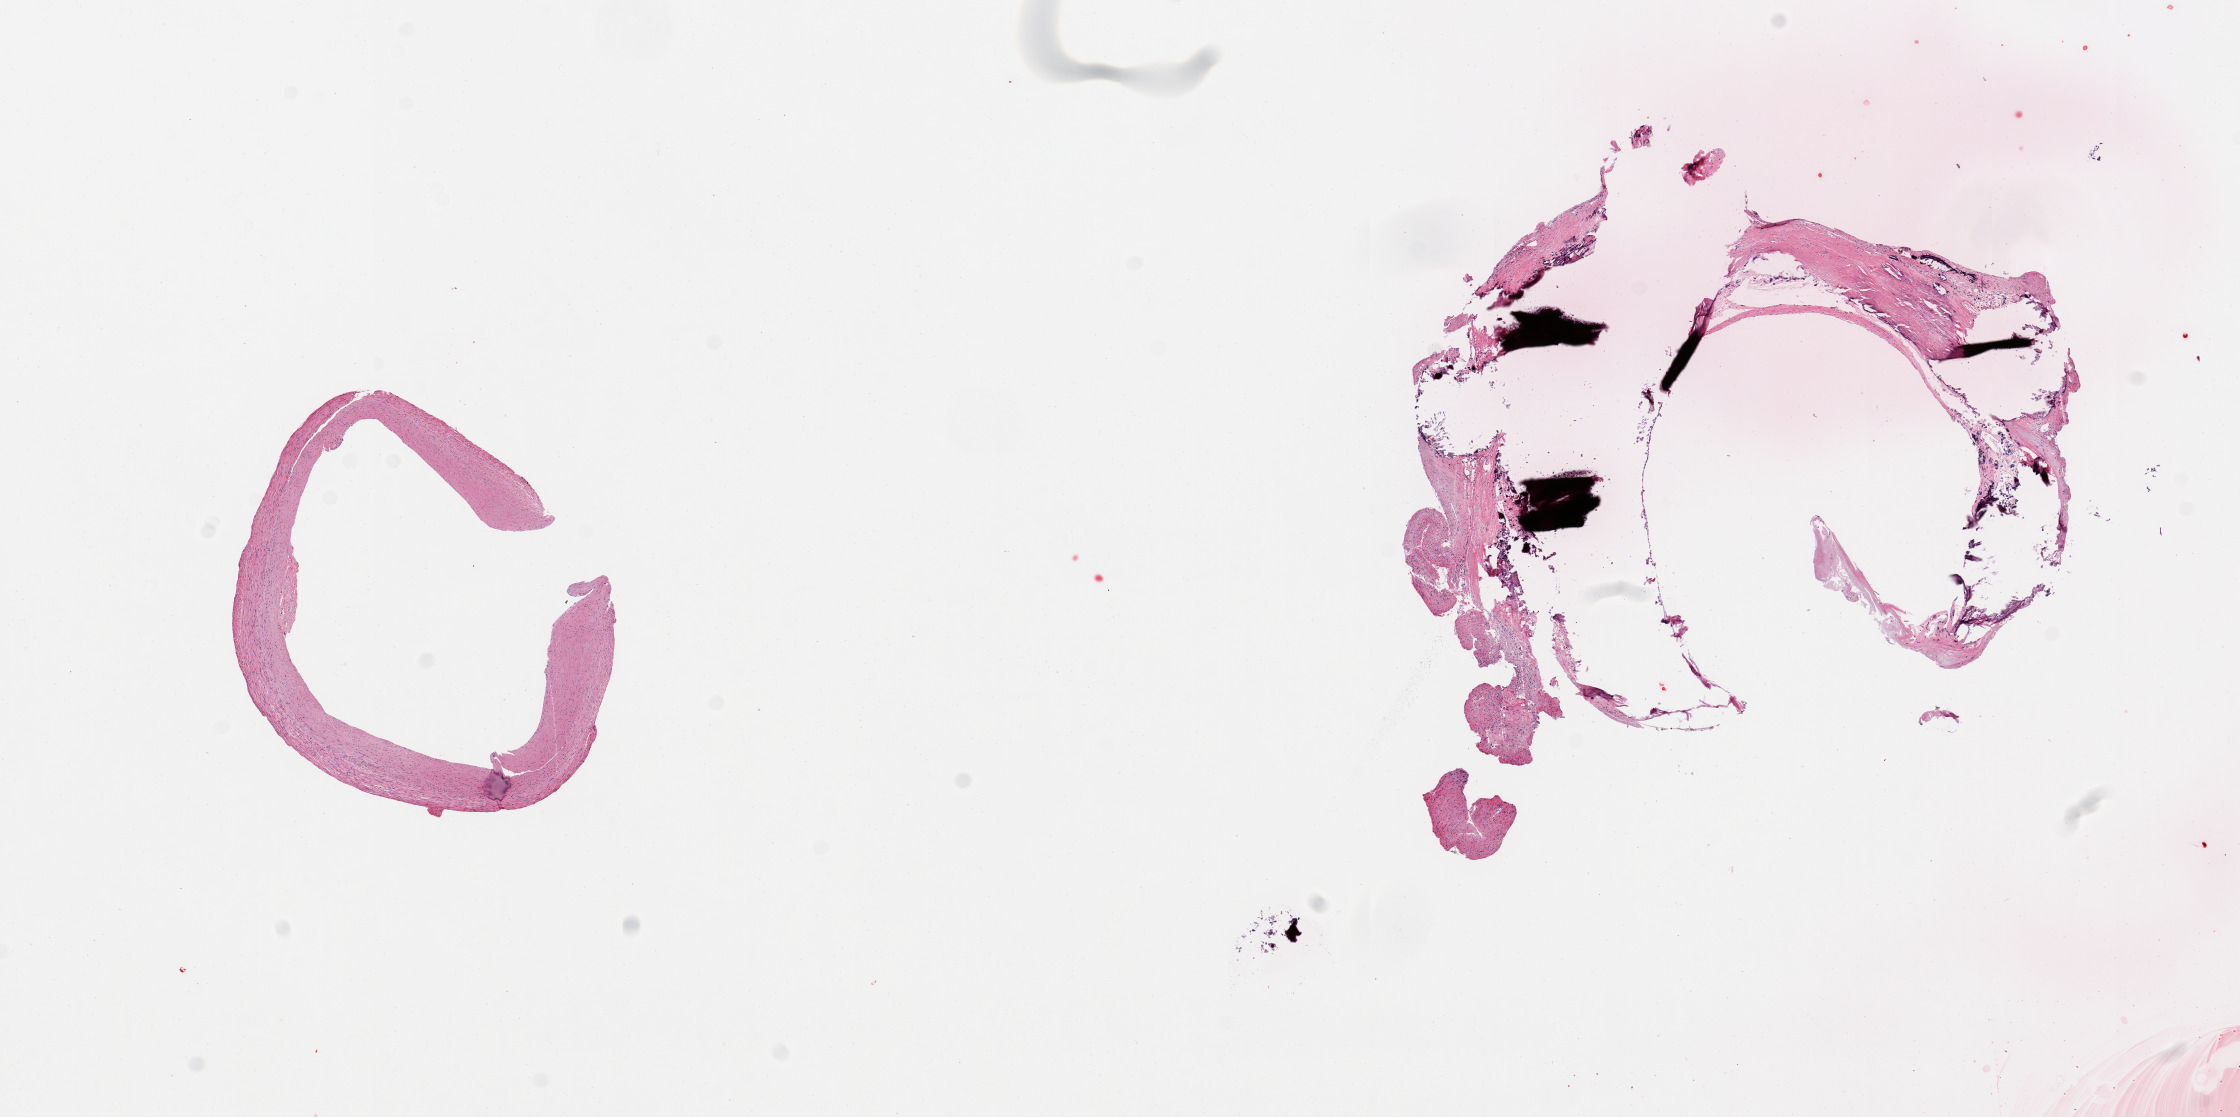
Whole-slide image, haematoxylin and eosin stain, low-resolution overview of the scanned area, about 17.7 x 8.8 mm, PAXgene-fixed, paraffin-embedded tissue, target tissue: coronary artery, tissue donor sample. Male donor.
Pathologist's review note for this sample: 2 pieces, subtotally occlusive calcifying atherosis, one section (shattered).